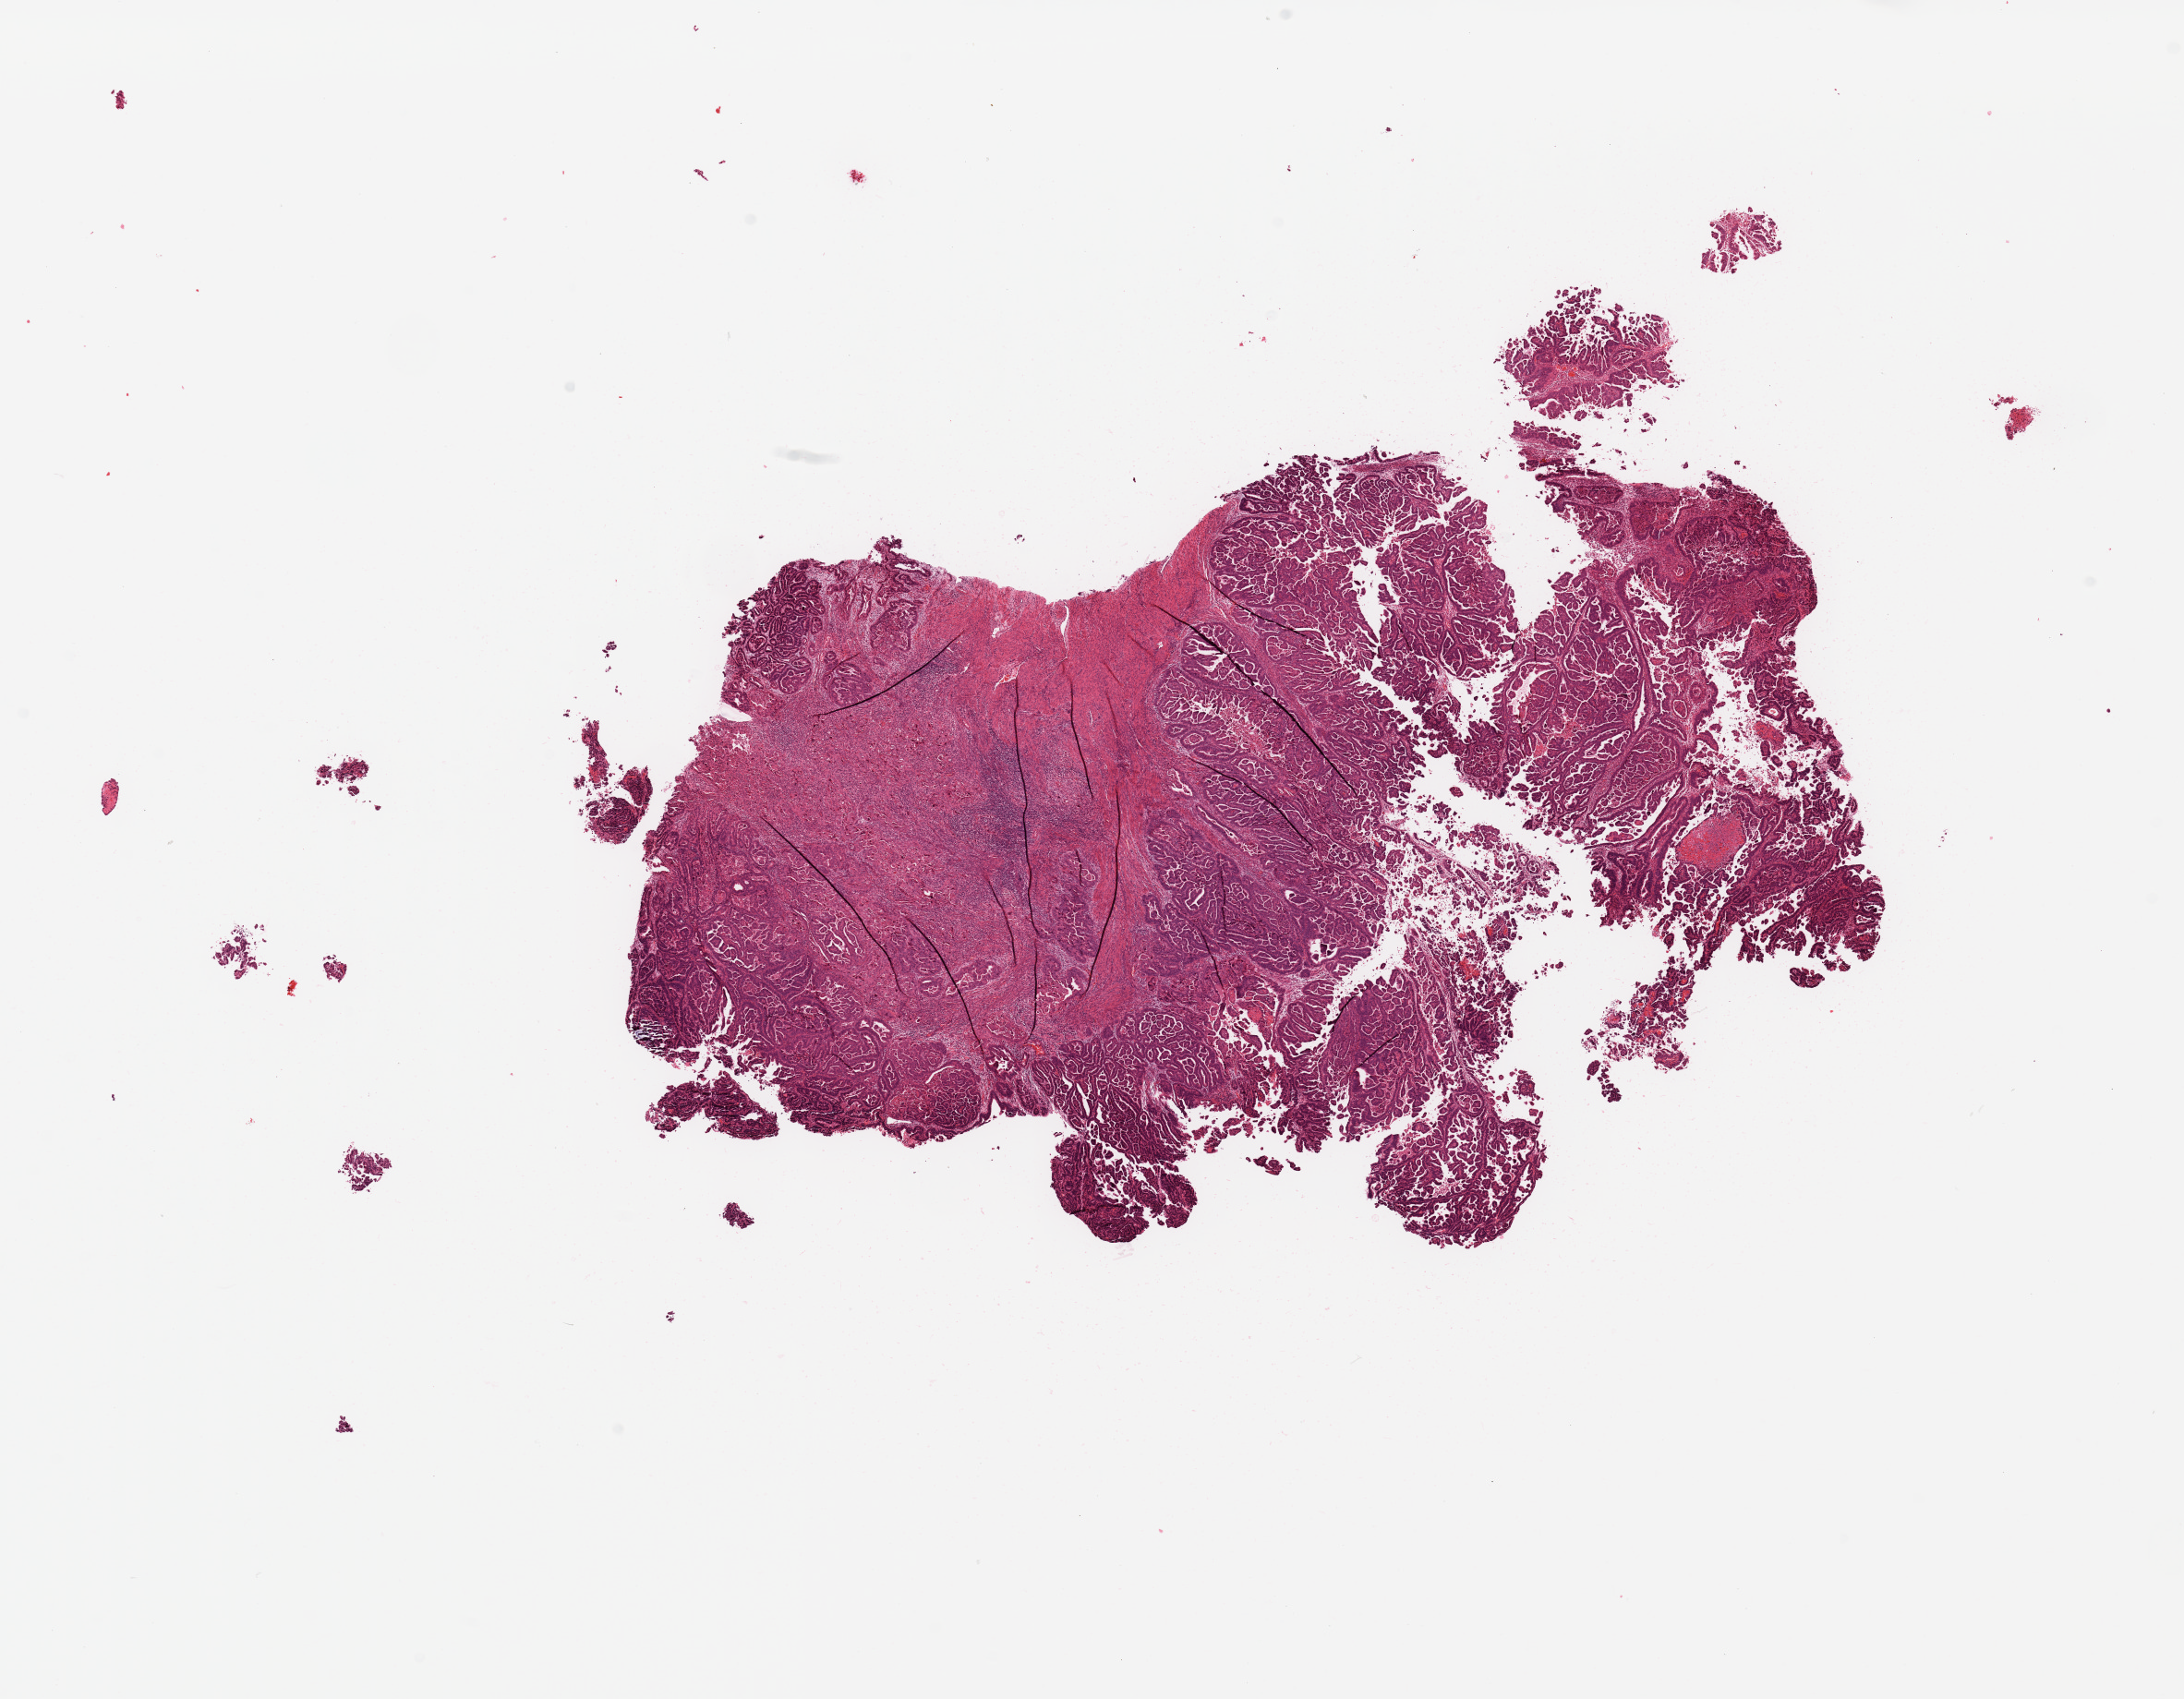
Digitized H&E-stained tissue section (whole slide), whole scanned area (about 18.7 x 14.6 mm) shown as a low-resolution overview, uterus, tumour tissue. 73-year-old female patient. Histologic grade: G3 (poorly differentiated).
- histologic diagnosis: Endometrioid adenocarcinoma, NOS
- AJCC pathologic stage: IIIC1